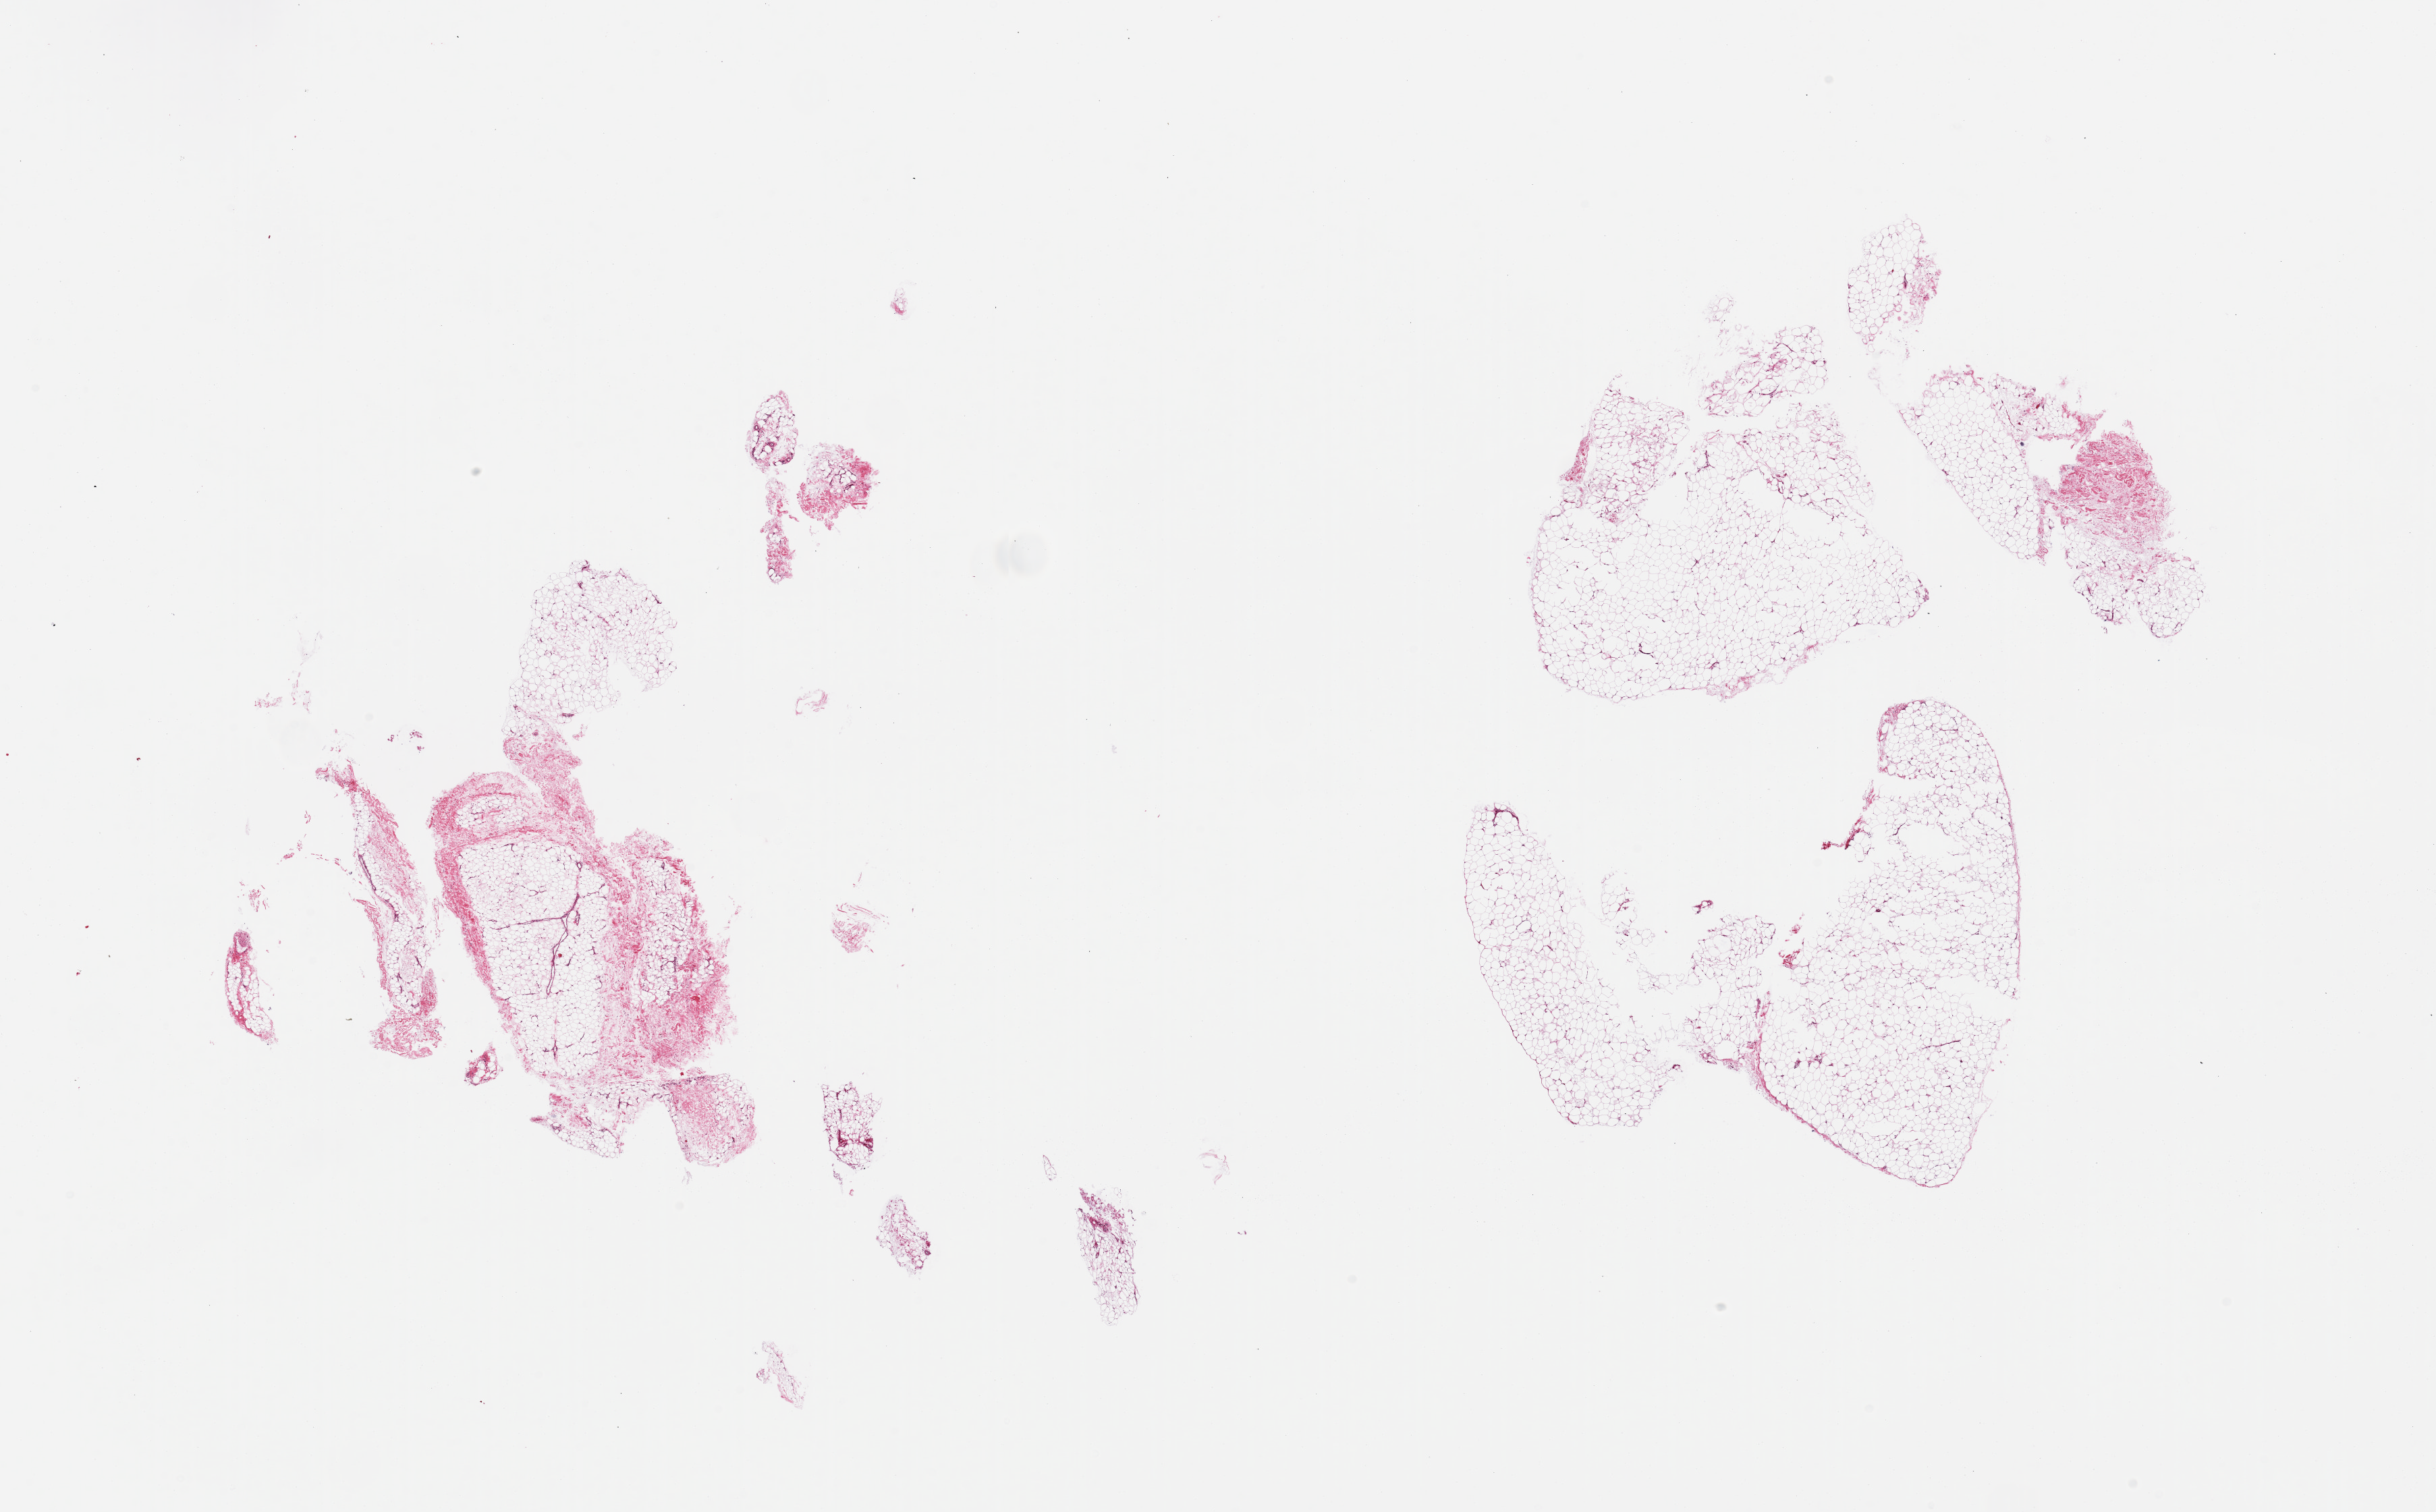
Whole-slide image, H&E stain — low-resolution overview of the scanned area, about 28.5 x 17.7 mm (acquisition: 20x scan), PAXgene-fixed paraffin-embedded (PFPE) section, target tissue: adipose tissue, tissue donor sample. Male donor.
Review note (as recorded): 2 pieces, ~15% fascia.